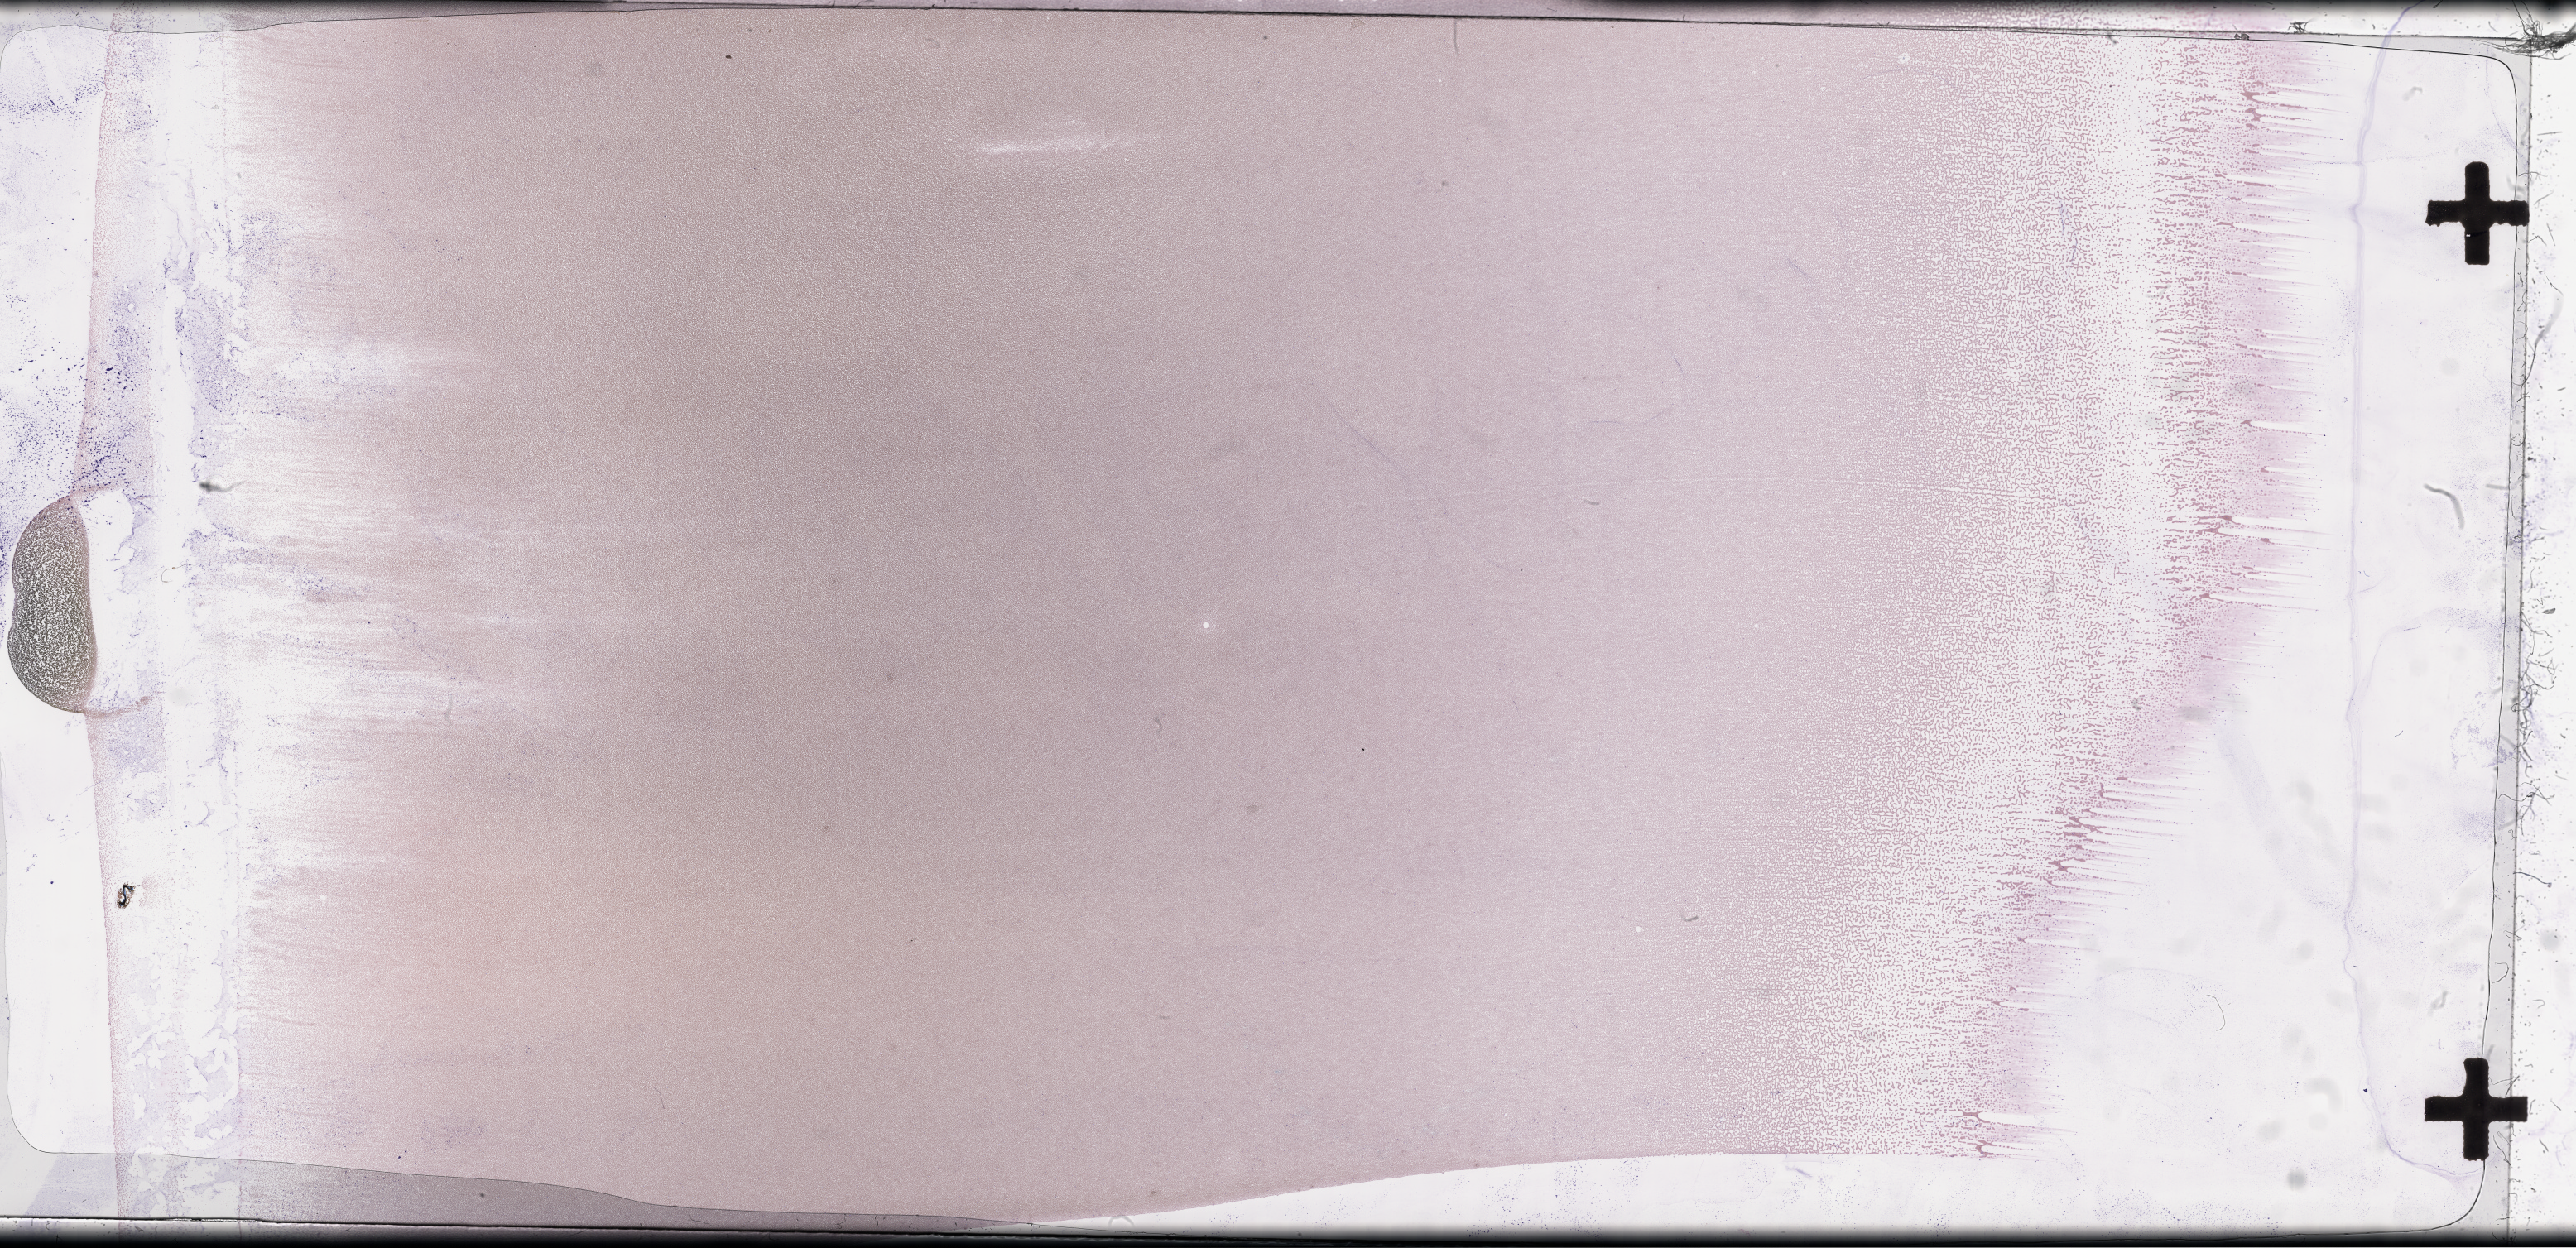
Whole-slide image of a whole blood smear, Wright–Giemsa stain, low-resolution overview of the scanned area, about 50.3 x 24.4 mm, collected on treatment. Patient sex: female.
Patient diagnosis: Plasma Cell Myeloma.